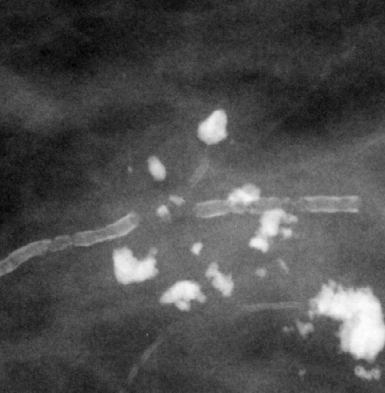
Region of interest cut from a scanned film mammogram (one marked finding); right breast; CC view; BI-RADS breast density category 1 (scale 1–4).
- Finding: calcifications, morphology coarse / pleomorphic, distribution clustered; BI-RADS assessment category 2; subtlety rating 5 on a 1 (subtle) to 5 (obvious) scale; pathology result (as recorded, not read from the image): benign.